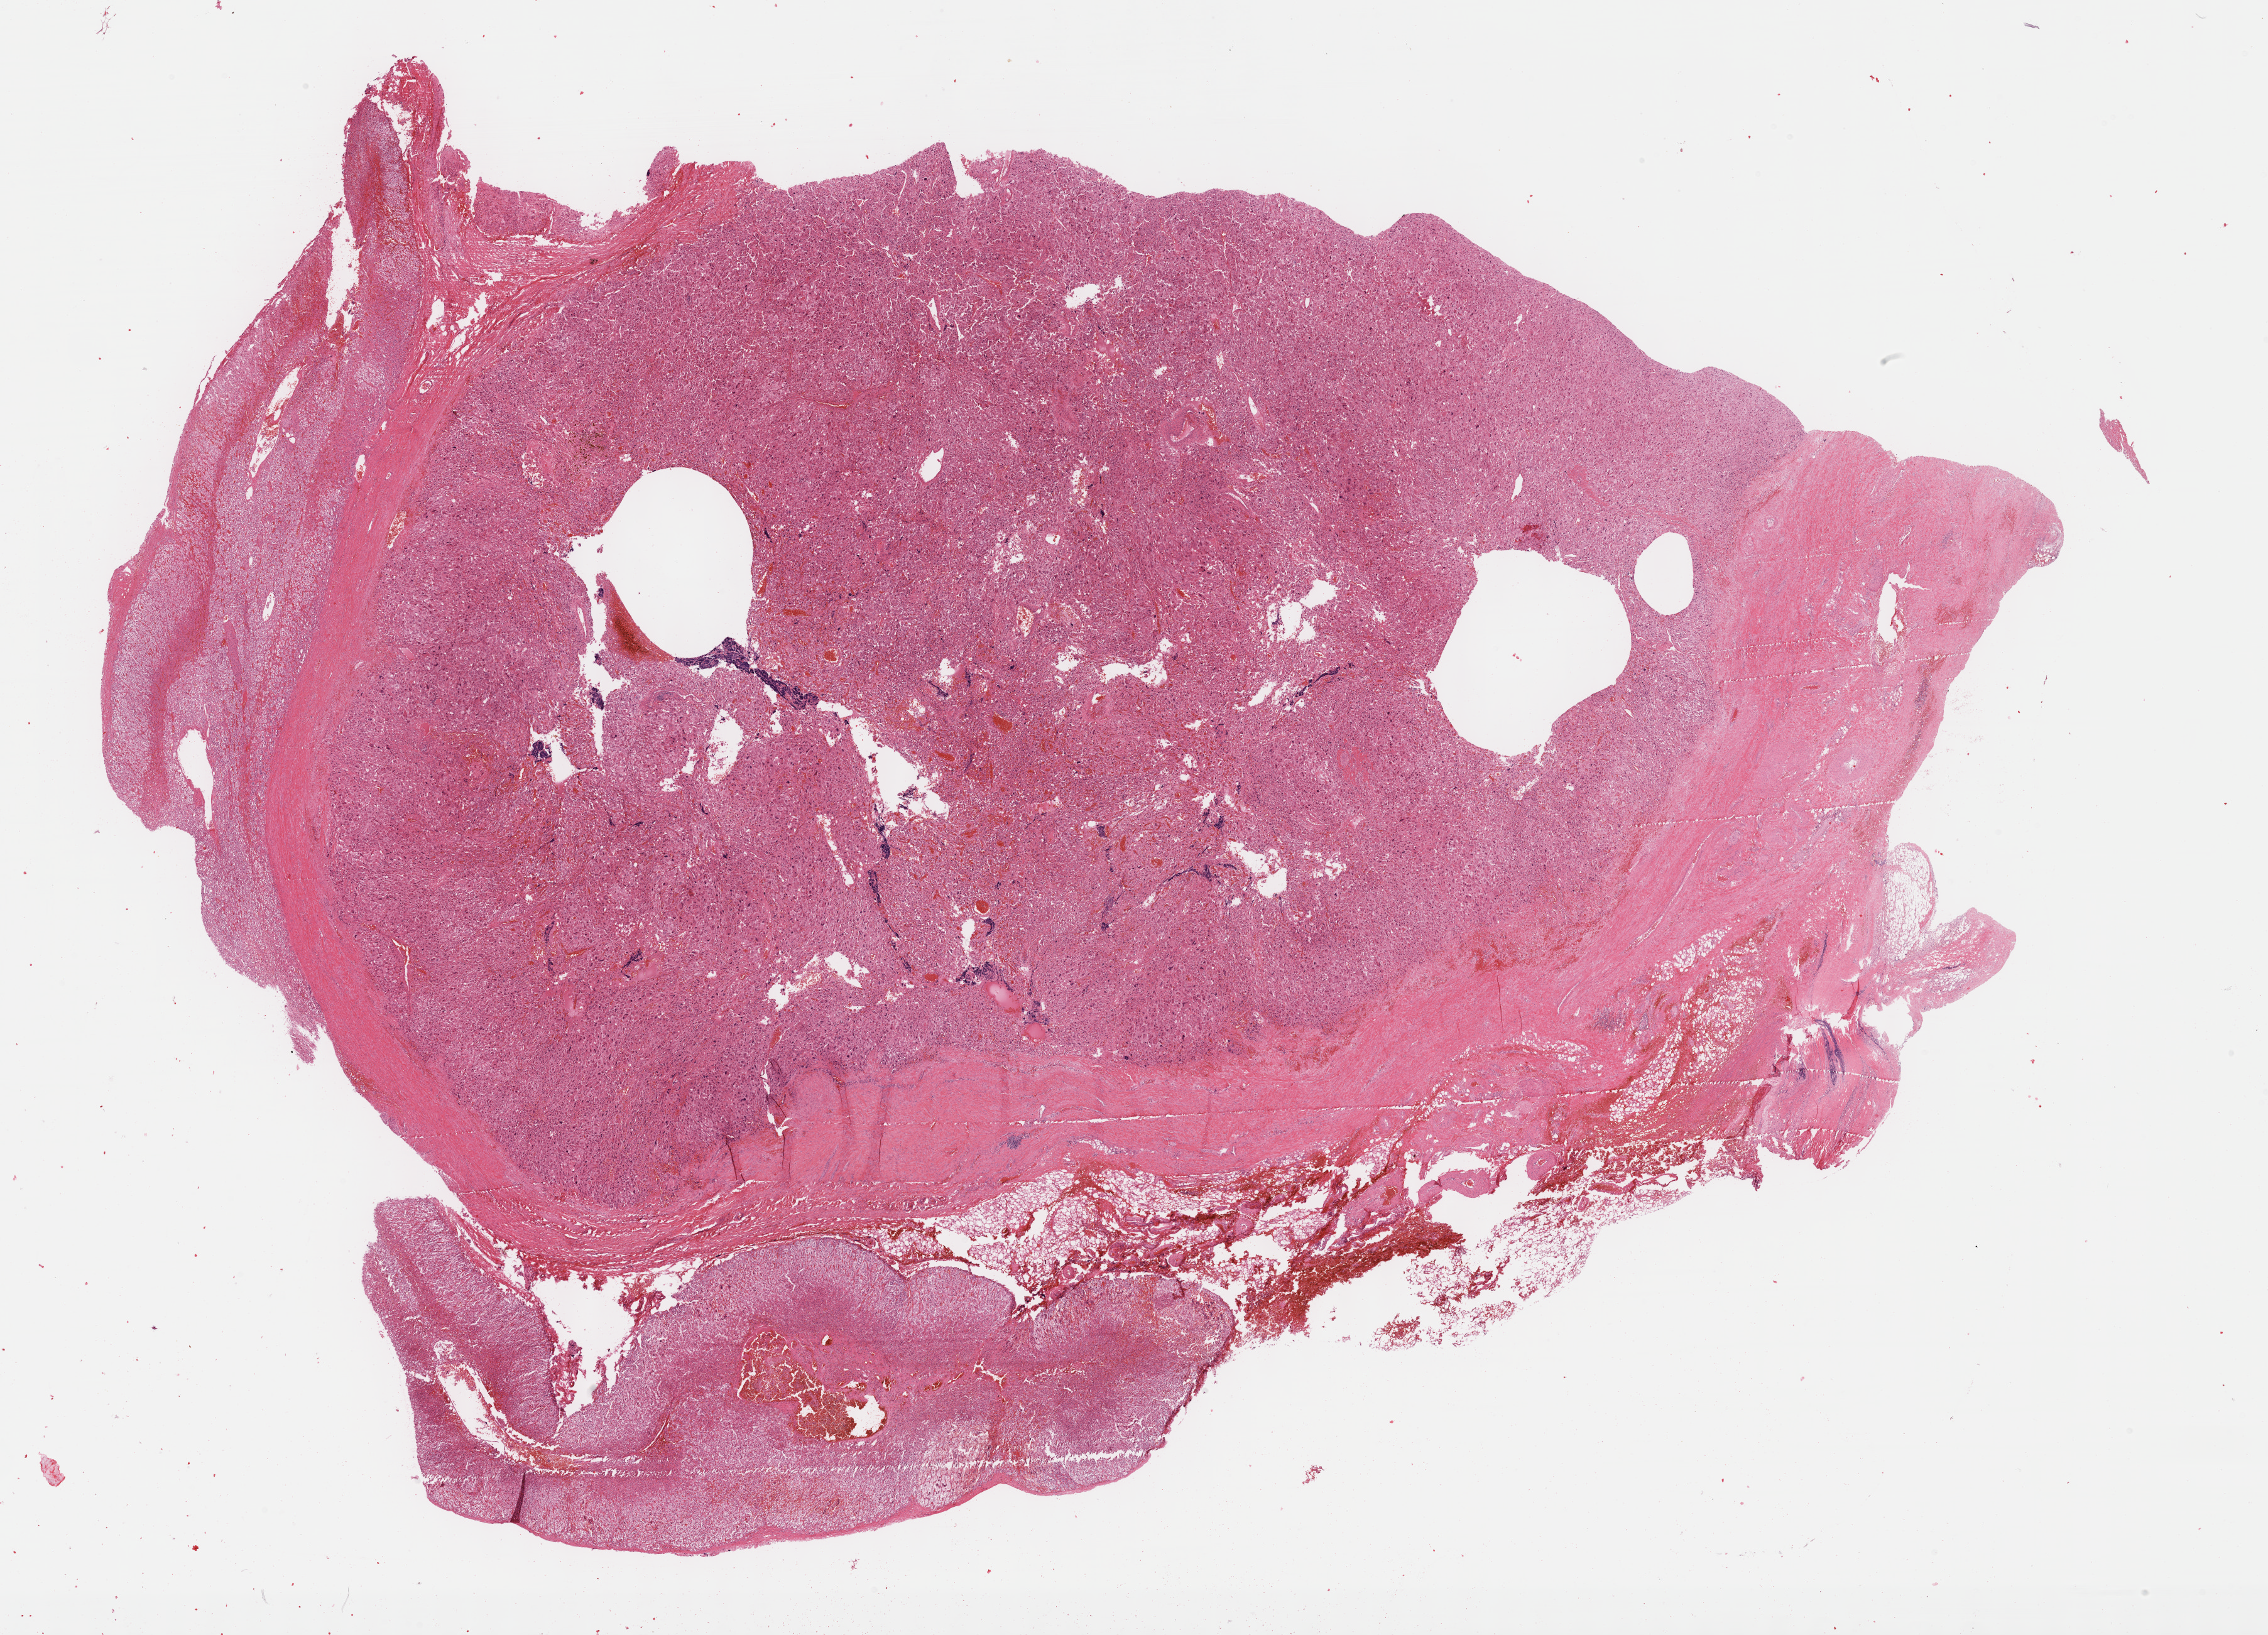
Digitized Hematoxylin and eosin (H&E) stained tissue section (whole slide), whole scanned area (about 29.2 x 21.1 mm, slide scanned at 40x) shown as a low-resolution overview, formalin-fixed paraffin-embedded (FFPE) diagnostic section, primary tumour sample from the adrenal gland. Patient: male, age at initial diagnosis 40 years.
- histologic diagnosis: Pheochromocytoma, malignant